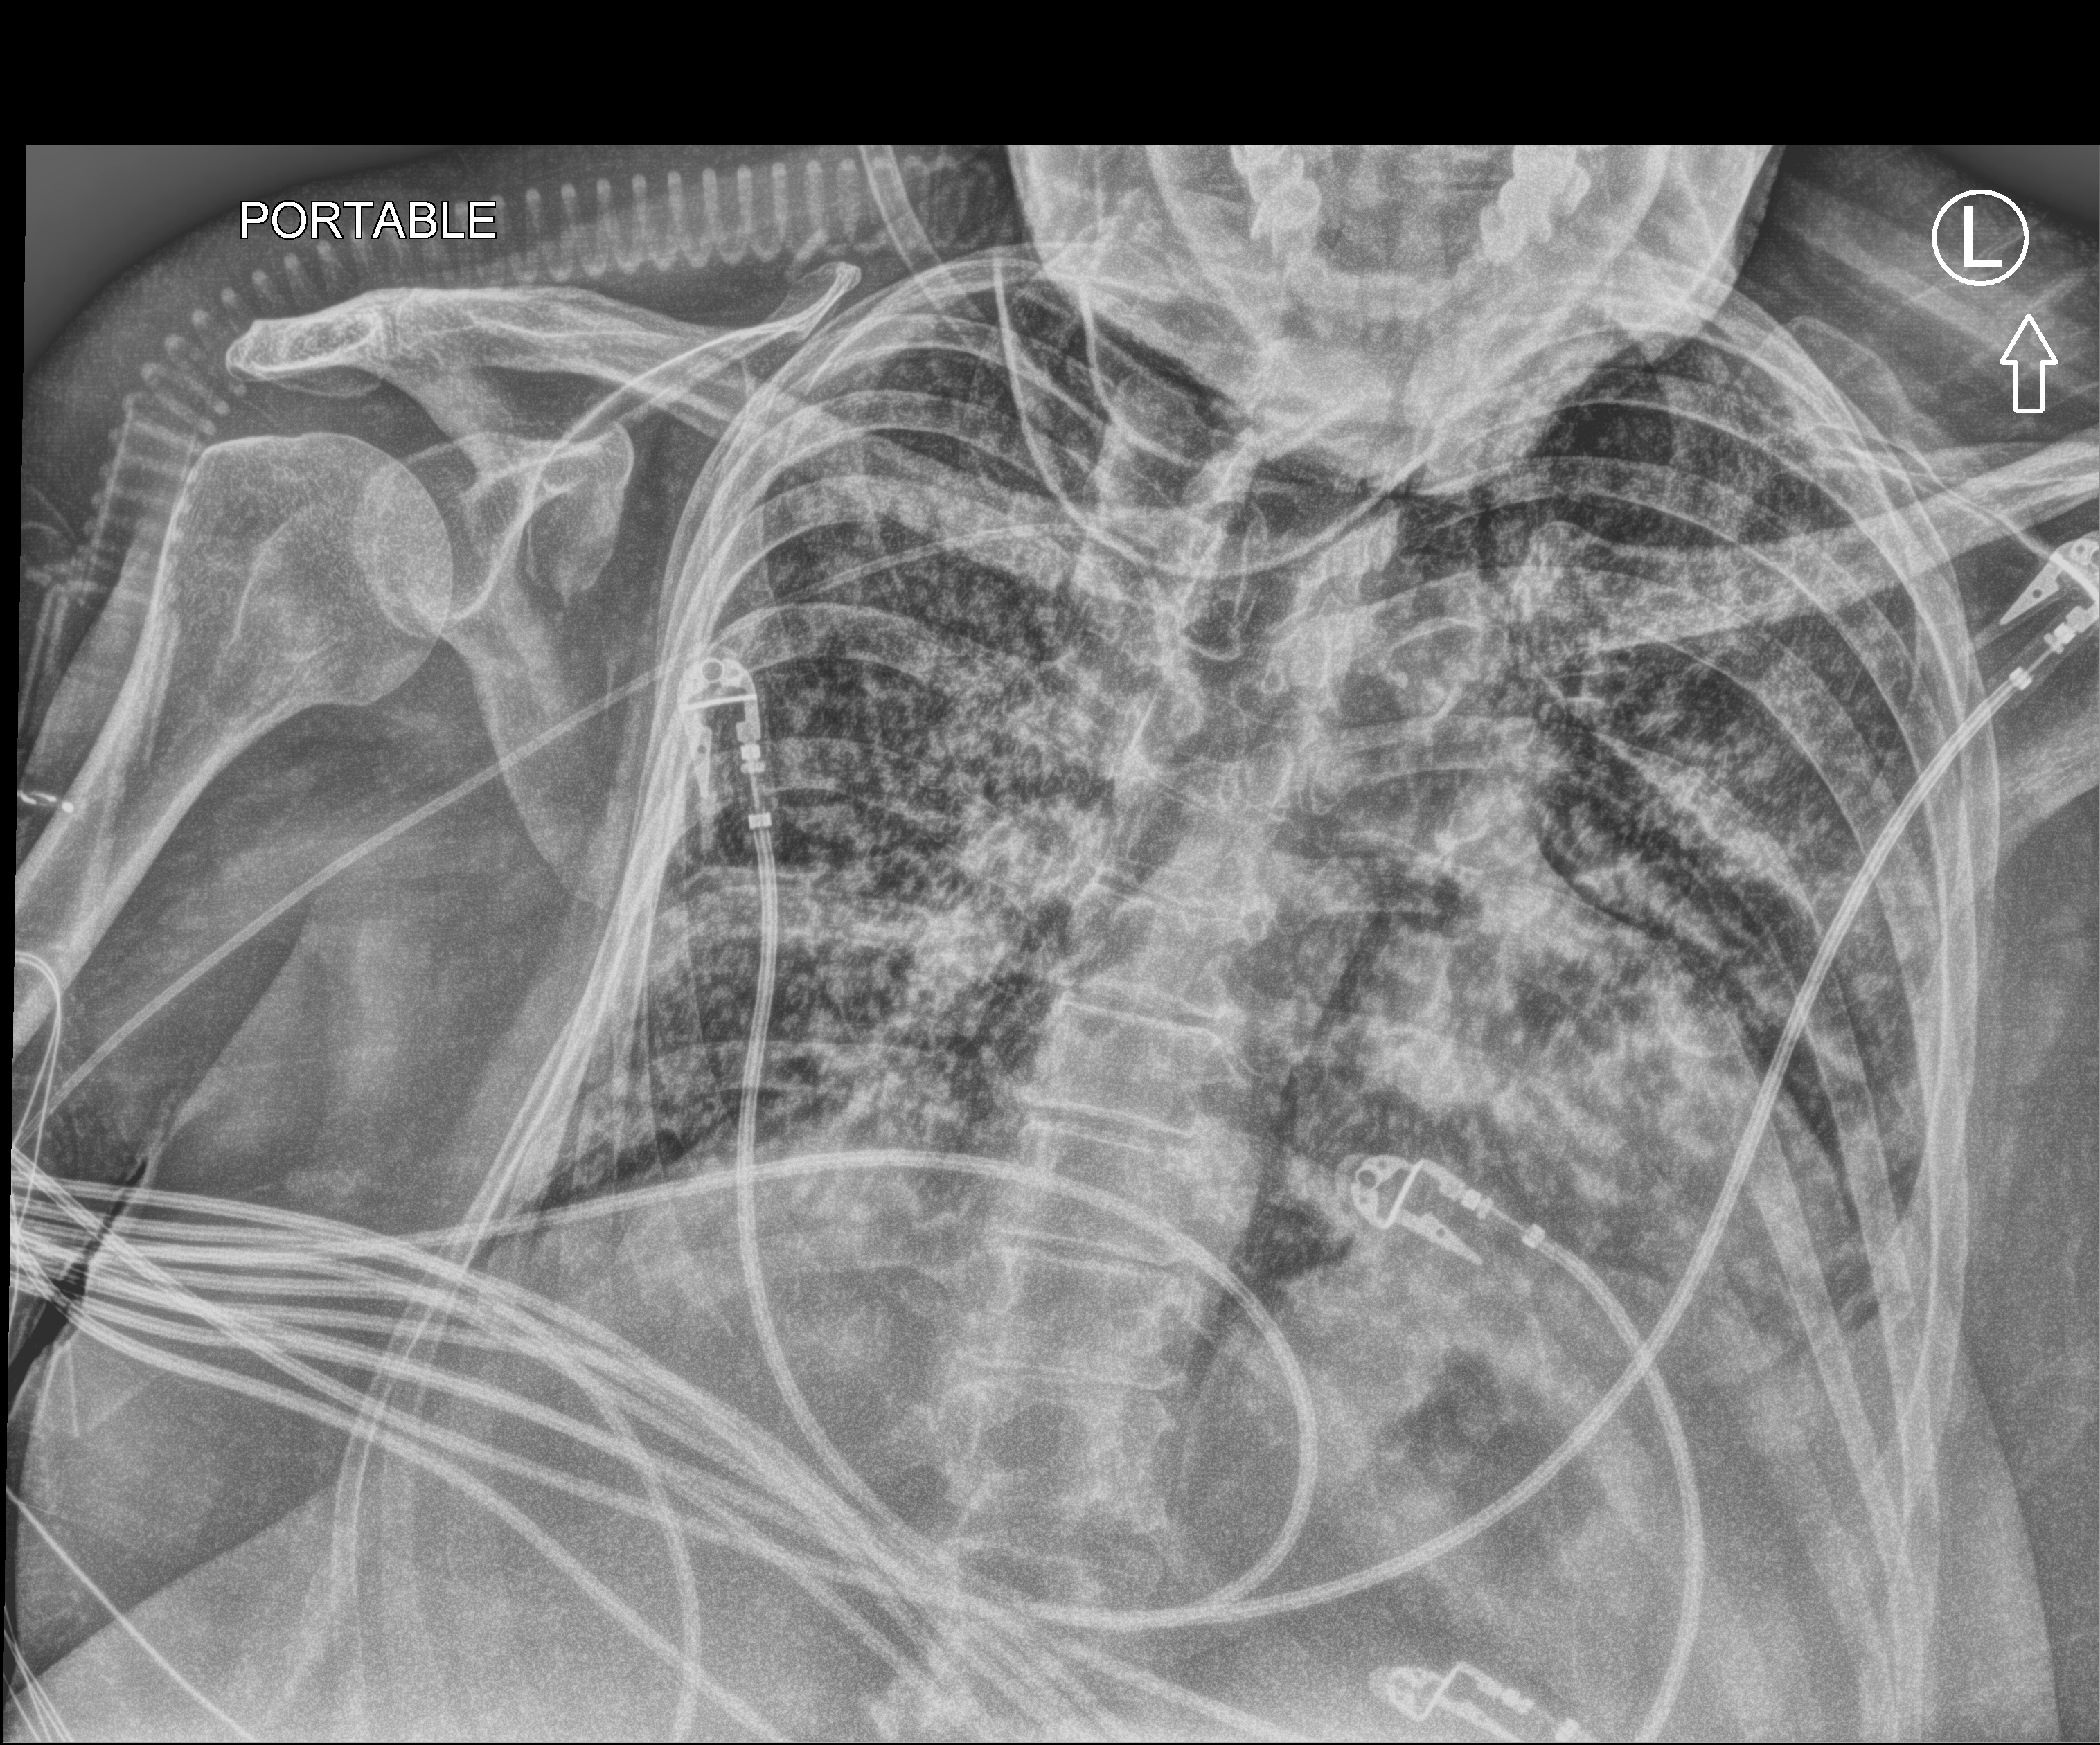
Chest X-ray (portable); anteroposterior (AP) projection. Female patient hospitalised with COVID-19, age 60–74 years.
Admission-level facts for this patient (not findings on this image; timing relative to this image not recorded): admitted to intensive care during this hospital stay: yes; diabetes (admission record): no.